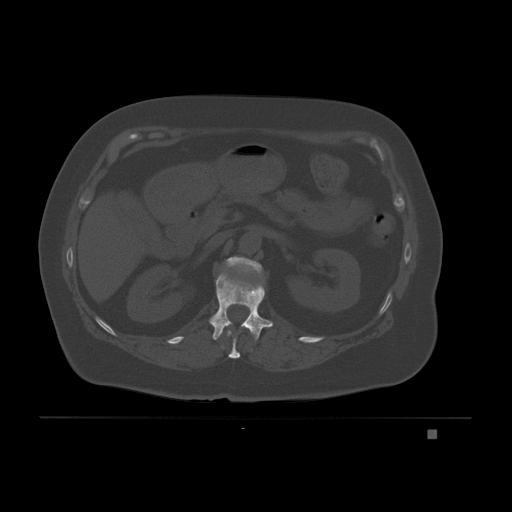
CT including the spine, one axial slice; slice 80 of 221 in the series (ordered by position); bone window (W 1800 / L 400 HU); 3 mm slice thickness; 512 × 512 image matrix. Patient: female, 63 years. From the clinical record (not read from this slice): primary cancer: breast.
Outlined on this slice (semi-automatic segmentation, software-assisted and operator-edited):
- L1 vertebra: bounding box (x1, y1, x2, y2) in pixels: (225, 256, 263, 285)
- T11 vertebra: (226, 330, 240, 359)
- T12 vertebra: (209, 270, 273, 341)